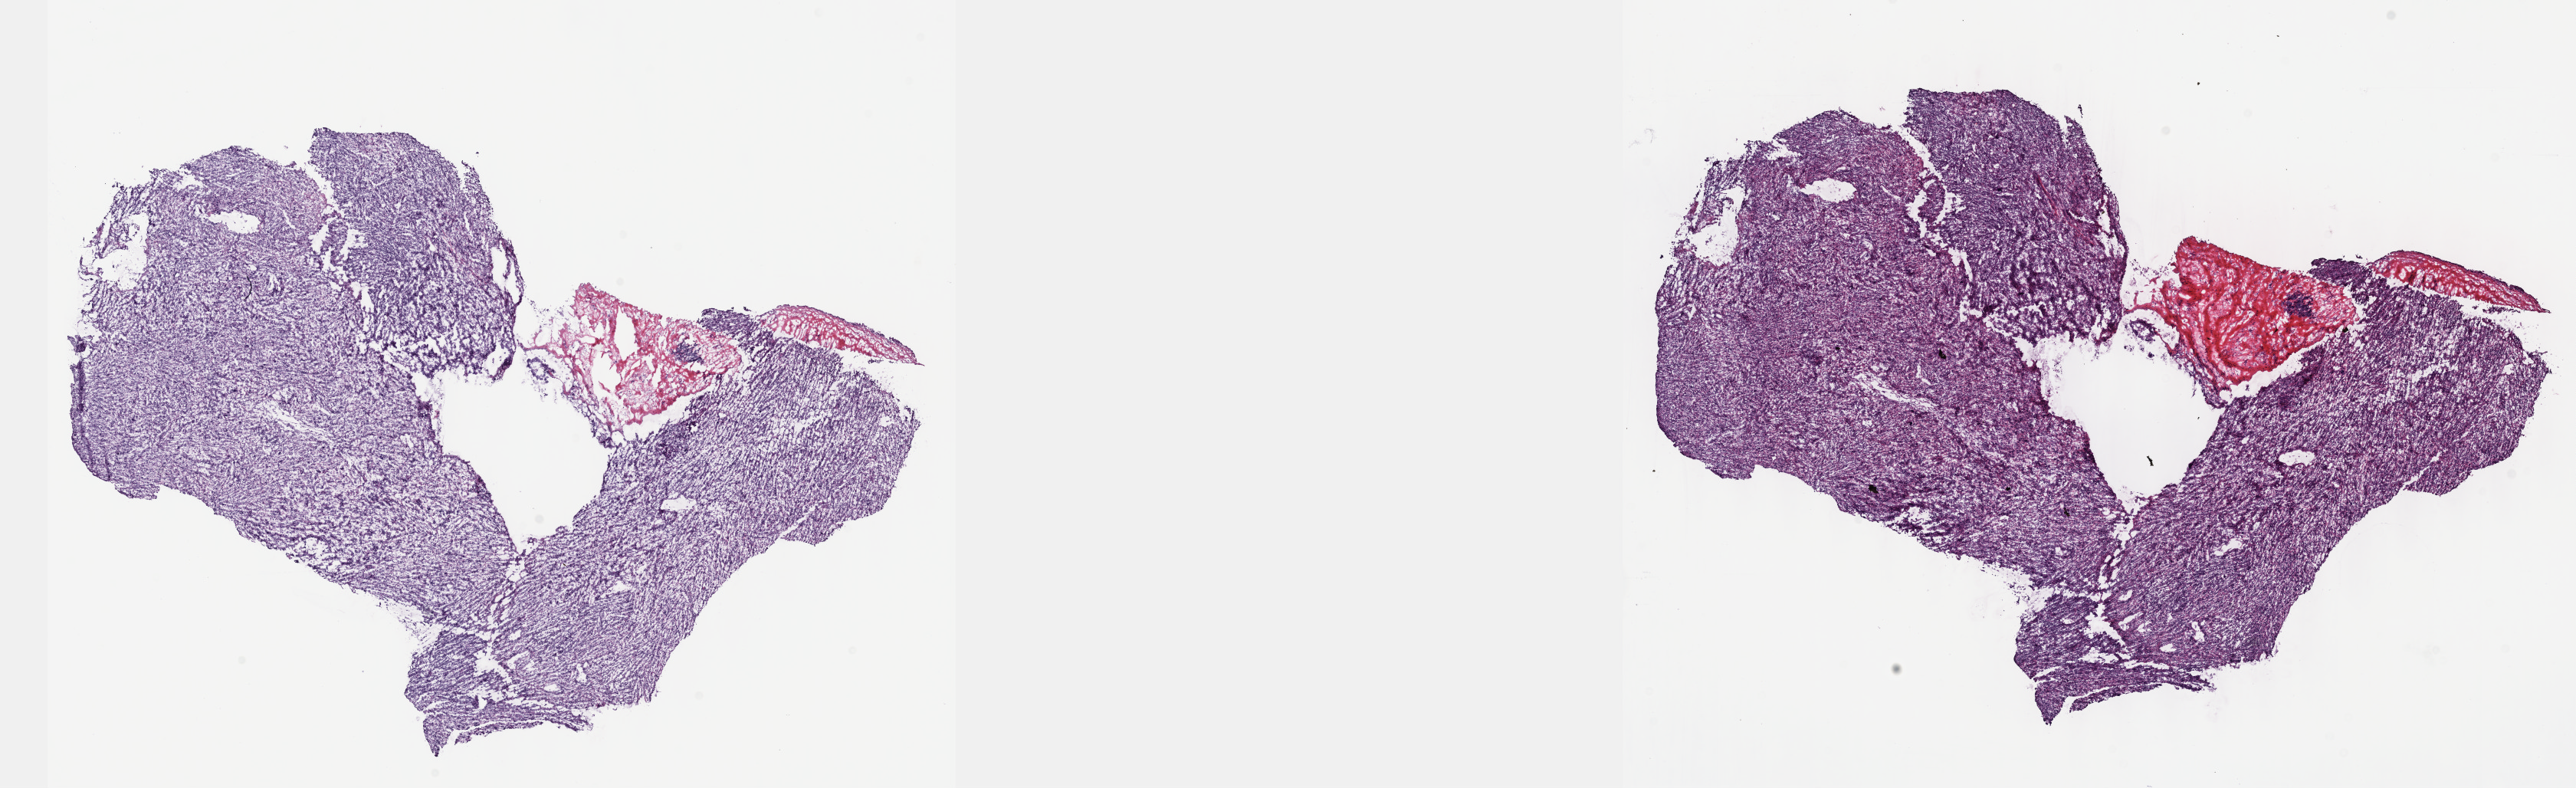
Whole-slide histology image, Hematoxylin and eosin (H&E) stained, whole scanned area (about 27.2 x 8.3 mm, from a 40x scan) shown as a low-resolution overview; frozen section from the top of the tissue portion; primary tumour sample from the connective, subcutaneous and other soft tissues. Patient: male, age at initial diagnosis 71 years. Slide review estimates, as recorded: tumour cells 95%, tumour nuclei 96%, normal cells 0%, stromal cells 5%, necrosis 0%. Infiltration values recorded for this section: lymphocyte infiltration 0%, monocyte infiltration 0%, neutrophil infiltration 0%.
Diagnosis: Undifferentiated sarcoma.